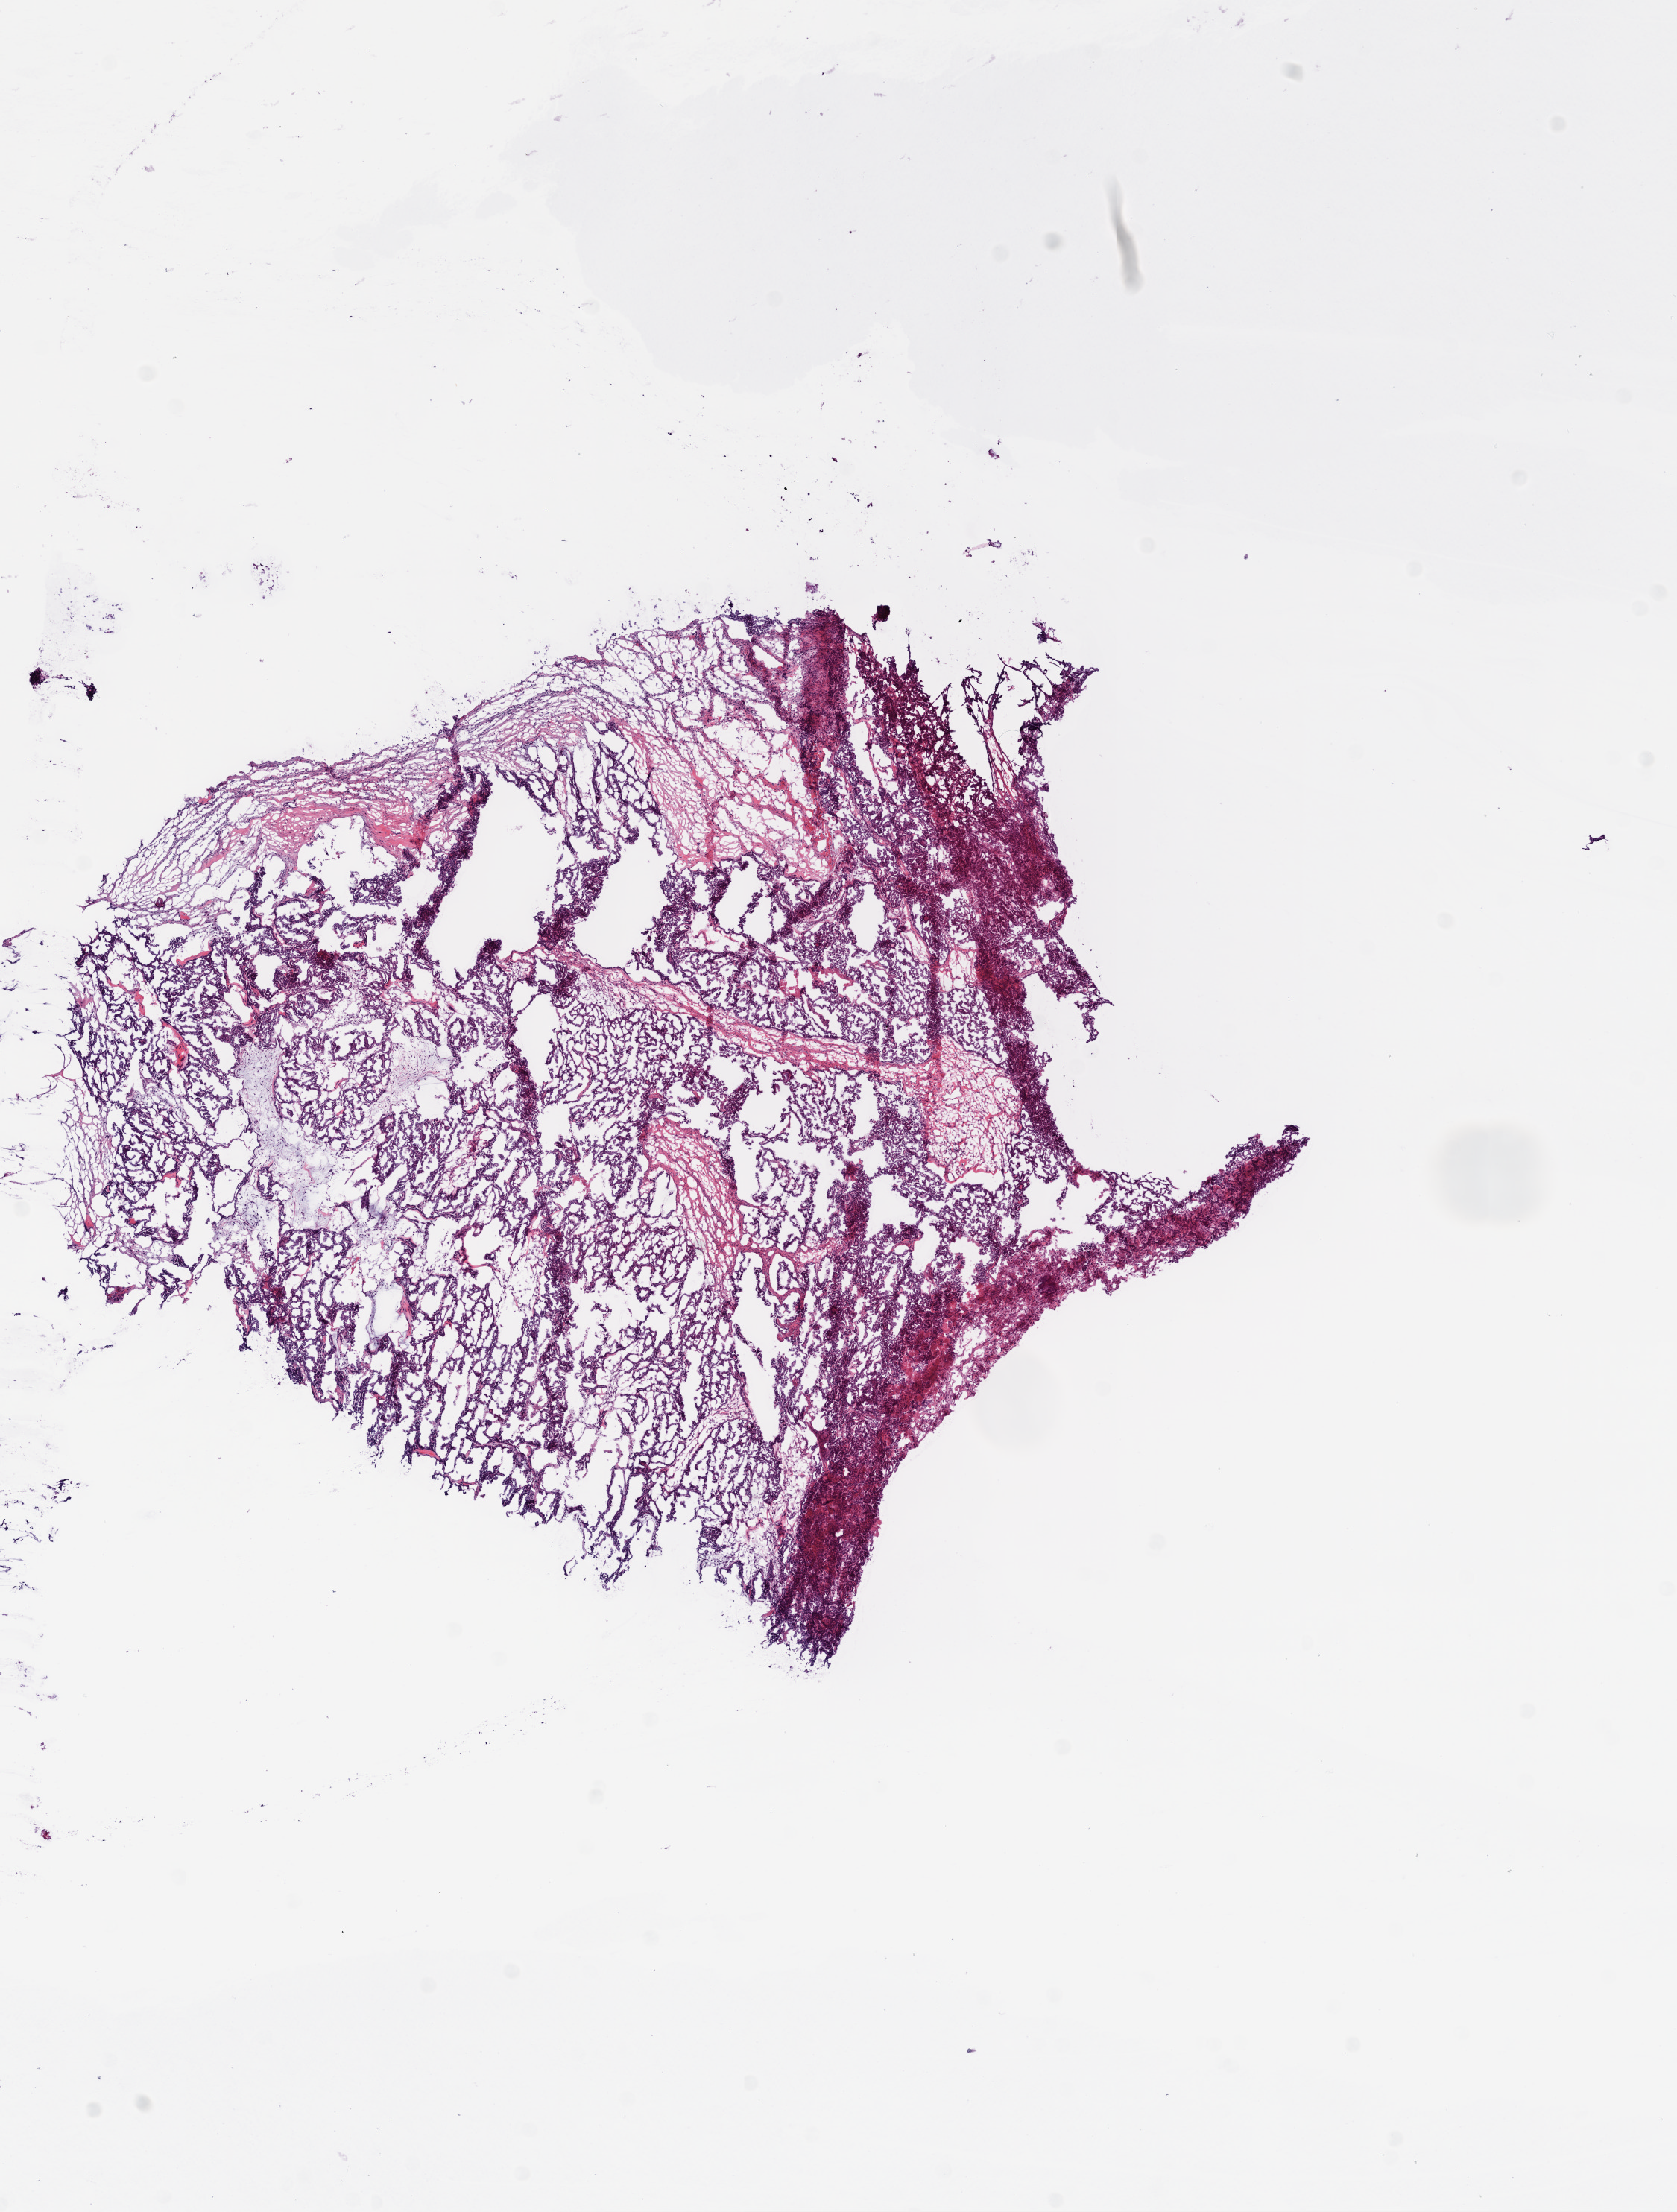
Digitized H&E-stained tissue section (whole slide), whole scanned area (about 9.0 x 11.9 mm, acquisition: 20x scan) shown as a low-resolution overview; frozen section; sample: primary tumour, ovary. Female patient; age at initial diagnosis 48 years. Histologic grade: G3 (poorly differentiated). Slide review estimates, as recorded: tumour cells 80%, tumour nuclei 90%, normal cells 0%, stromal cells 15%, necrosis 5%.
- pathologic diagnosis: Serous cystadenocarcinoma, NOS
- FIGO stage: IIIC
- laterality: bilateral